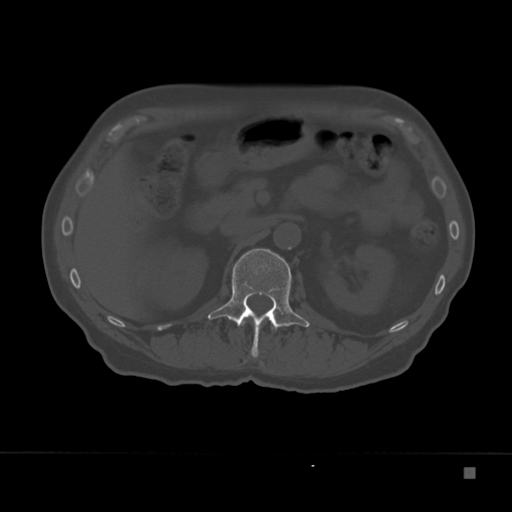
CT including the spine, one axial slice; slice 113 of 332 in the series (ordered by position); bone window (W 1800 / L 400 HU); 1.5 mm slice thickness; 512 × 512 image matrix. Patient: male, 72 years. Case-level facts recorded for this patient, not image findings: primary cancer: skeletal.
Annotated regions visible in this slice (semi-automatically segmented with operator editing):
- L1 vertebra: bounding box (x1, y1, x2, y2) in pixels: (208, 249, 310, 358)
- T12 vertebra: (243, 322, 275, 330)